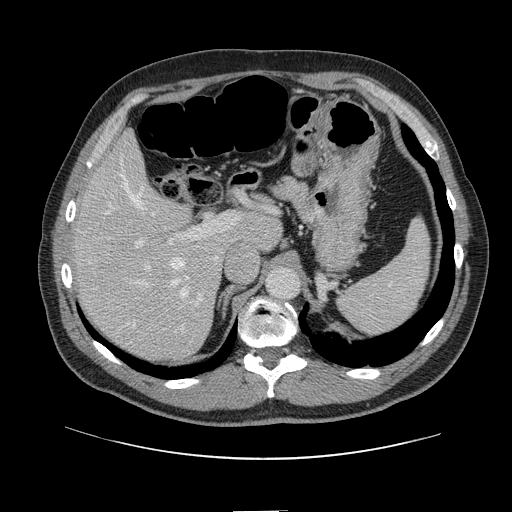
Contrast-enhanced abdominal CT, one axial slice. Intravenous contrast given. Soft-tissue window (W 400 / L 40 HU). 2.5 mm slice thickness. 512 × 512 image matrix, field of view 412 × 412 mm. Male patient, age 66 years. From the clinical record (not read from this slice): diagnosis: colorectal cancer liver metastases, imaged before liver resection; multiple liver metastases: no; largest metastasis: 3.5 cm; disease in both lobes: no.
Annotated regions visible in this slice (expert manual segmentation):
- hepatic veins: bounding box <104,159,189,327> (left, top, right, bottom; pixels)
- liver: <76,136,279,360>
- planned liver remnant (the part of the liver to remain after resection): <75,136,279,305>
- portal vein (with intrahepatic branches): <134,213,239,308>